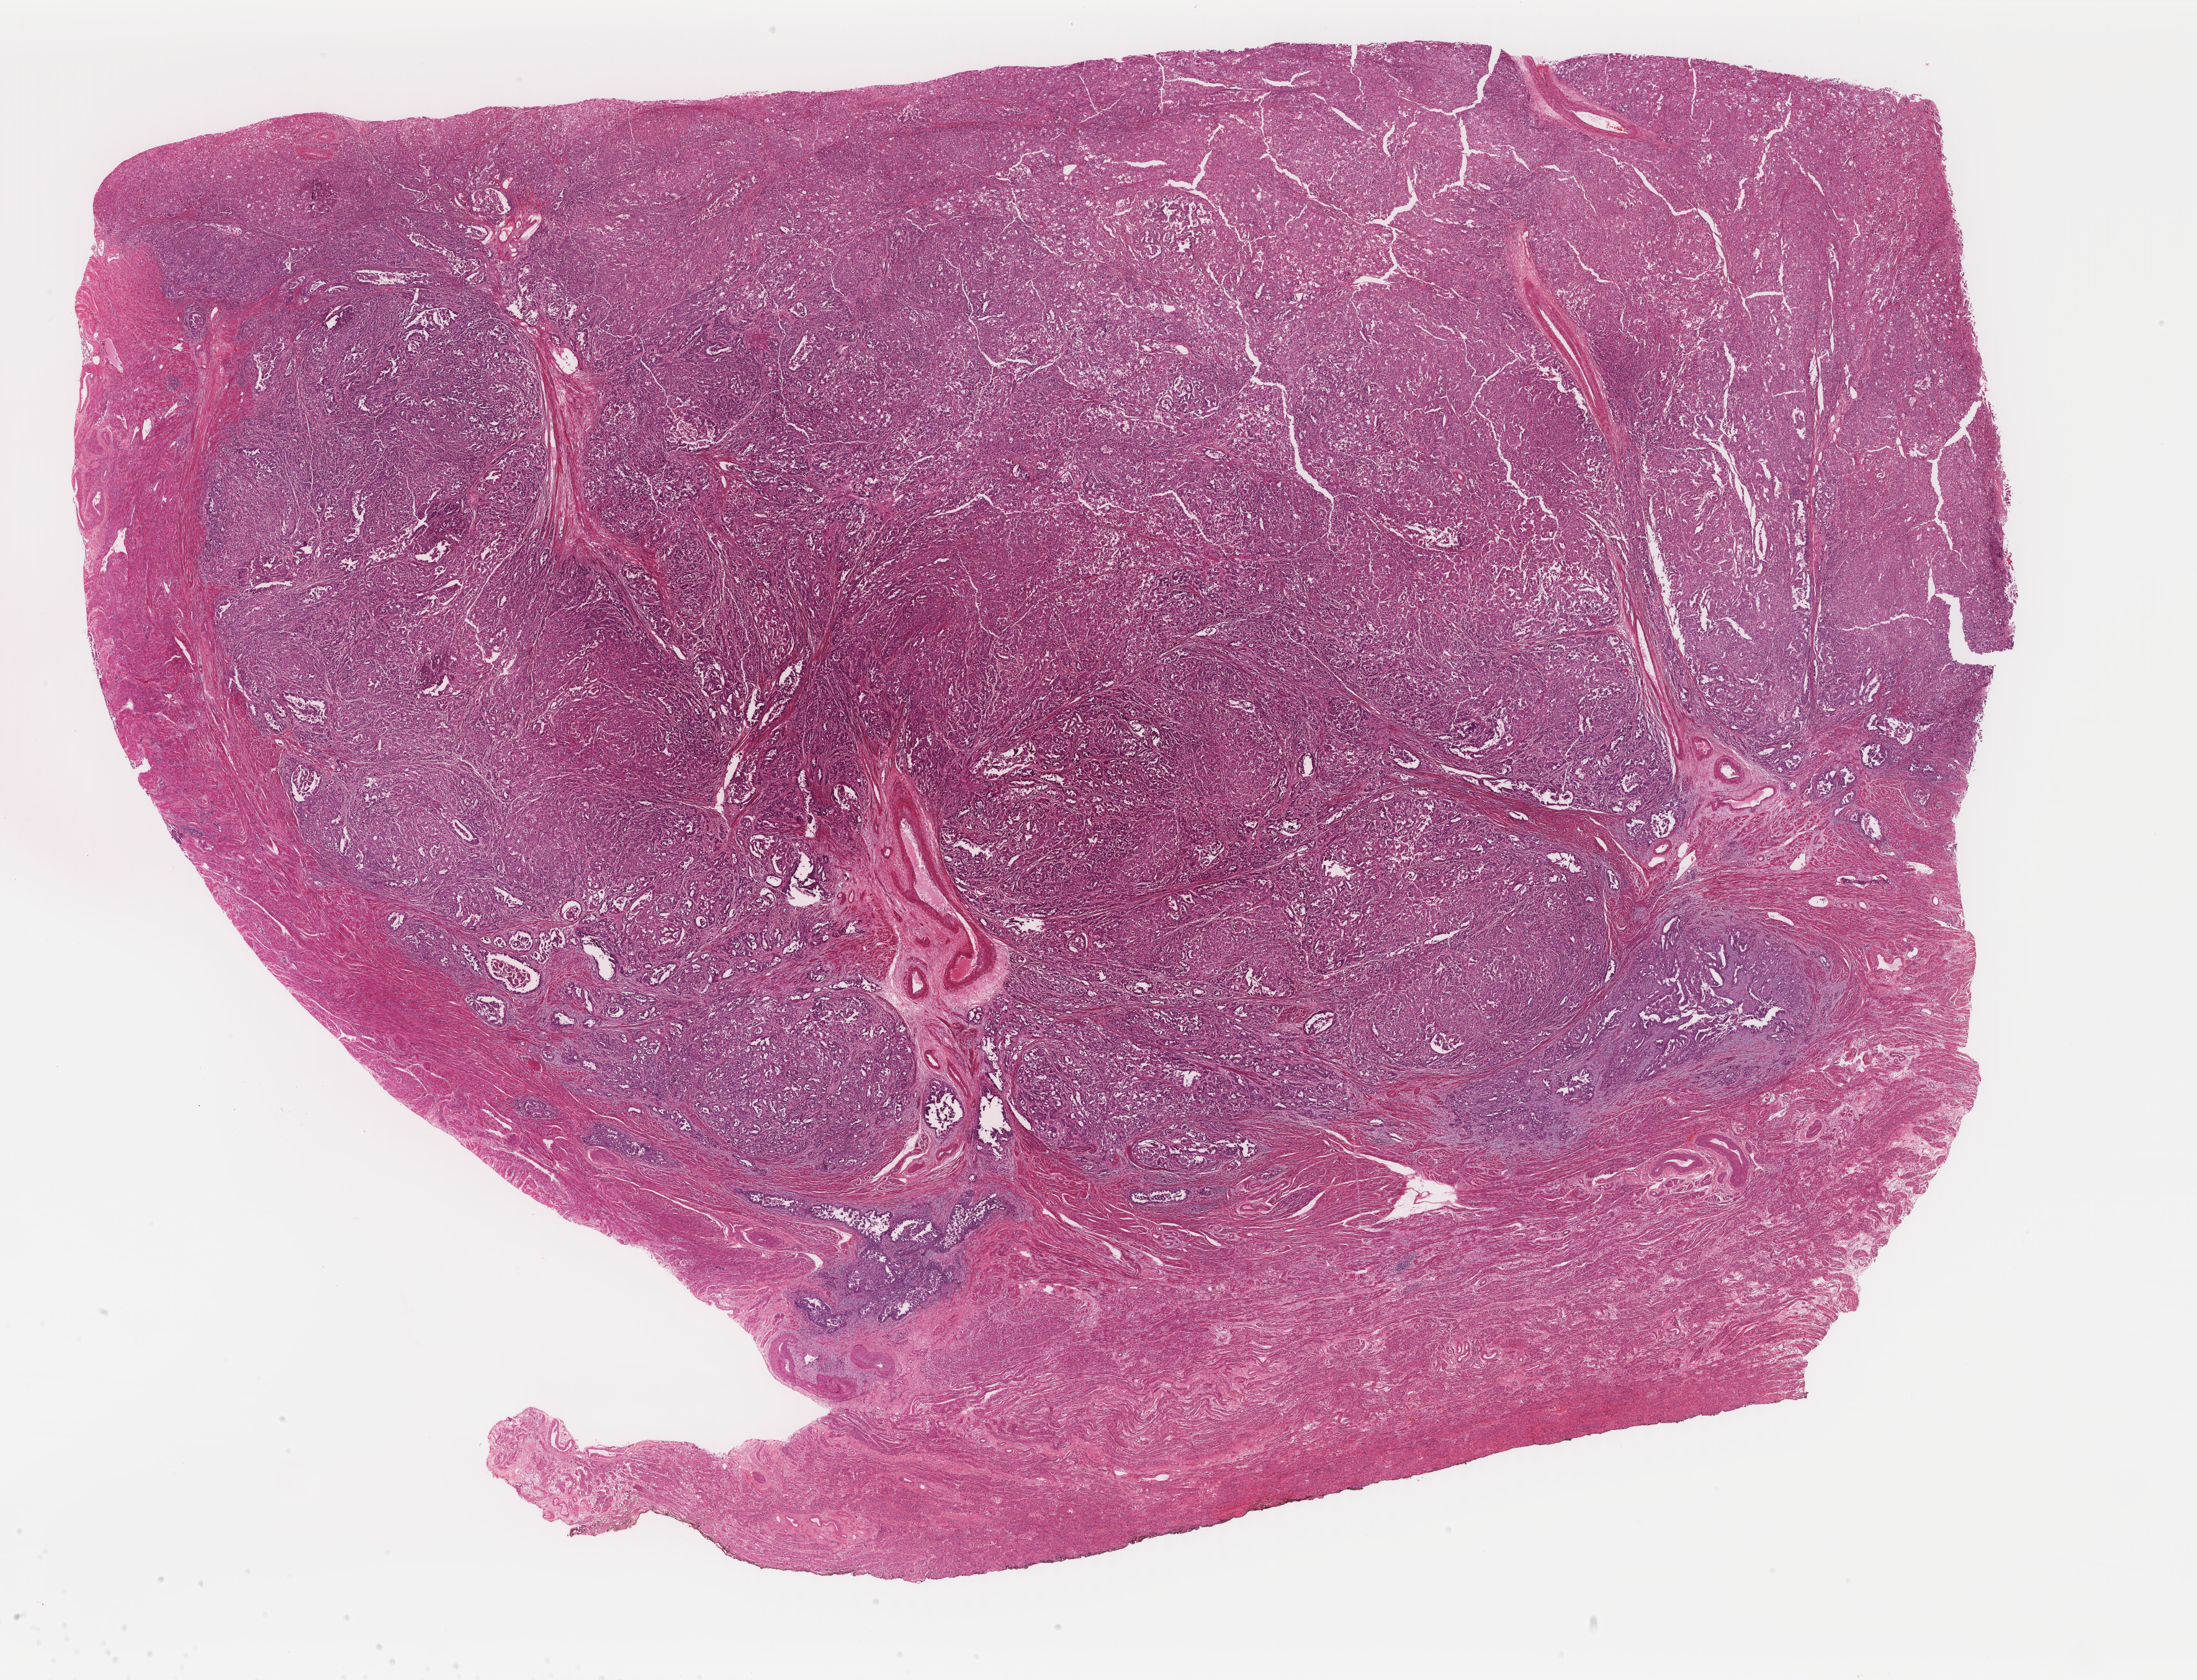
Digitized H&E tissue section (whole slide) — low-resolution overview of the scanned area, about 28.1 x 21.5 mm; FFPE section; uterus, primary tumour sample. Female, age 74 years at initial diagnosis. Histologic grade: G3 (poorly differentiated).
FIGO stage: IB. Histologic diagnosis: Serous cystadenocarcinoma, NOS (endometrium).